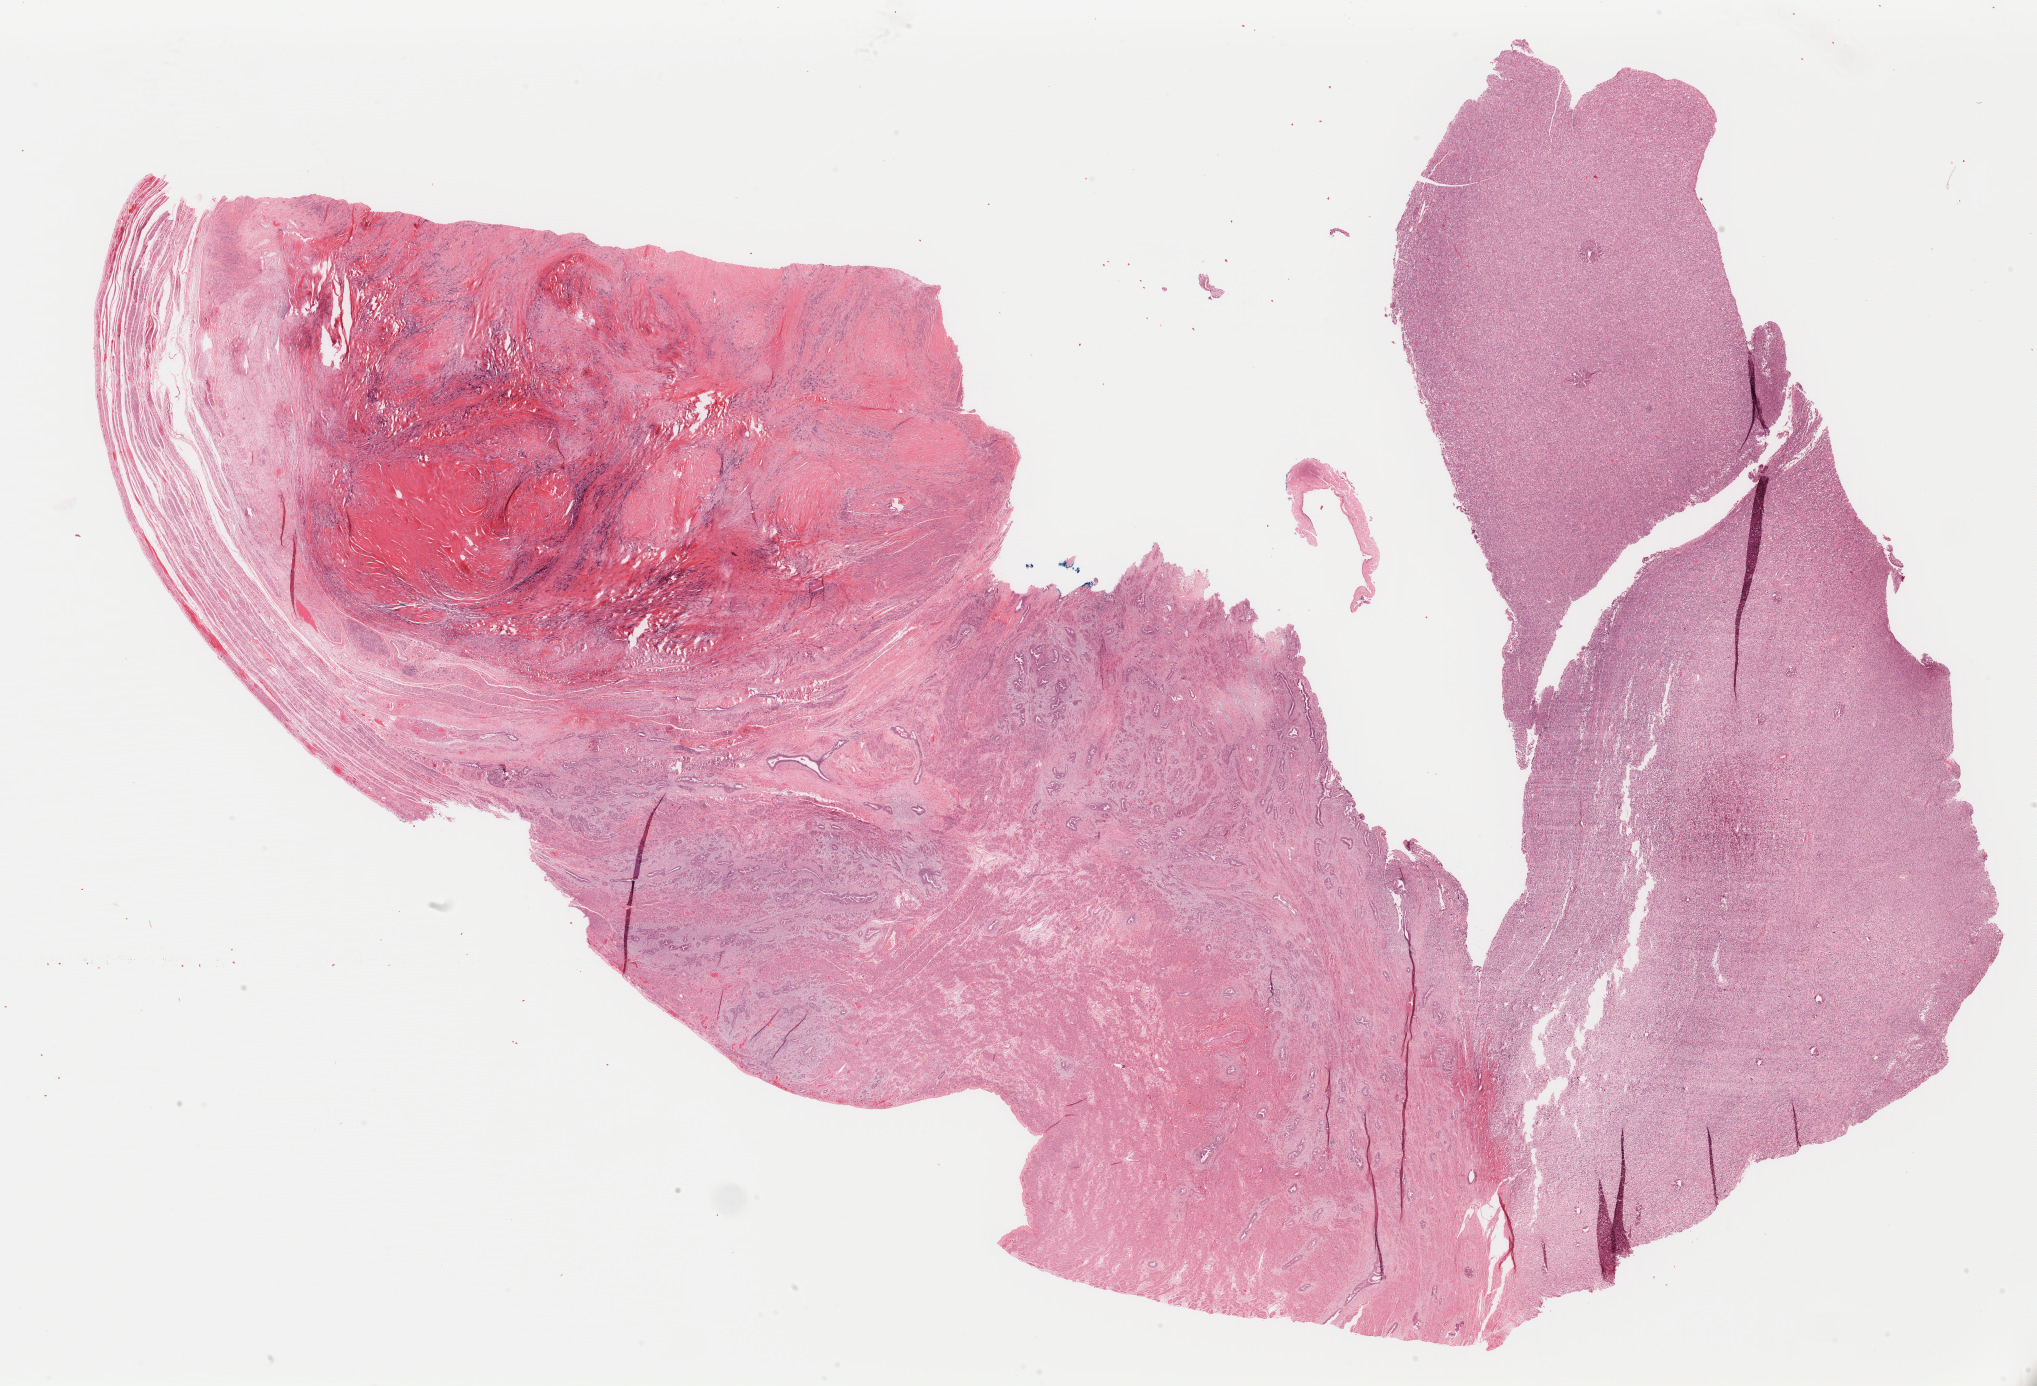
Hematoxylin and eosin (H&E) stained whole-slide image — shown as a low-resolution overview of the whole scanned area (about 32.1 x 21.9 mm), formalin-fixed paraffin-embedded (FFPE) diagnostic section, uterus, primary tumour sample. Female, age 87 years at initial diagnosis.
Diagnosis: Mullerian mixed tumor (endometrium). FIGO stage: IIB.